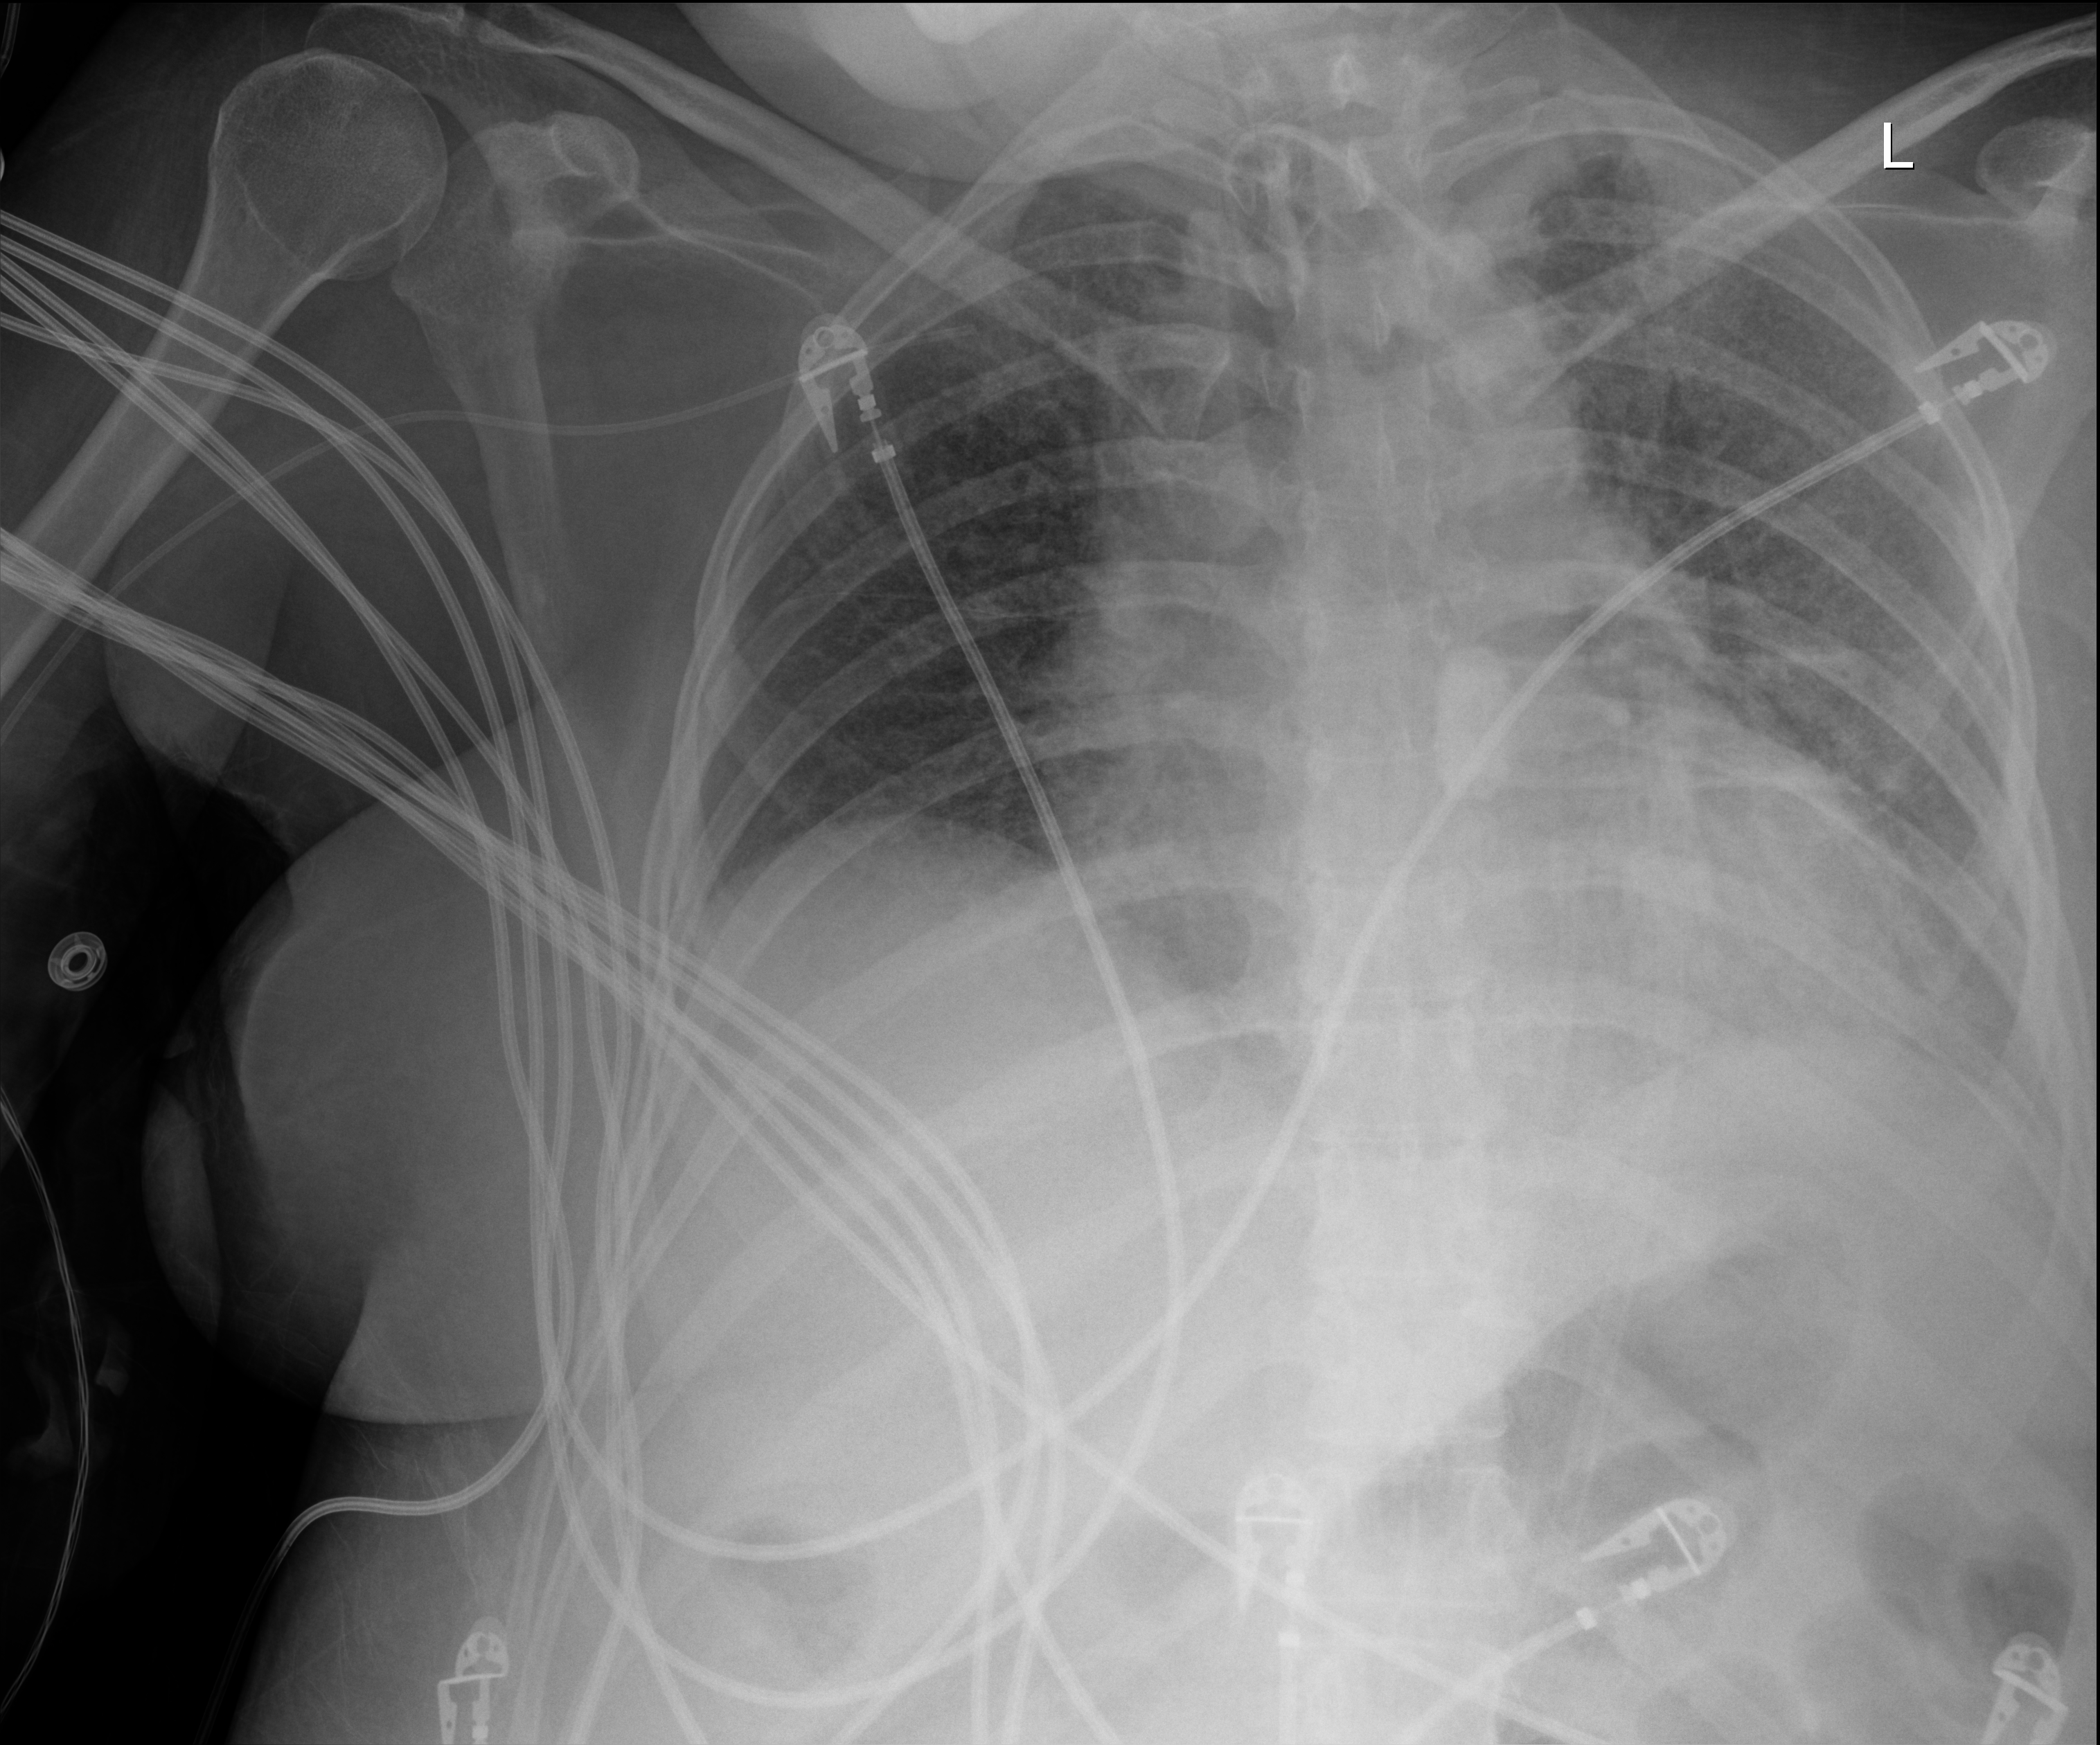
Chest X-ray (portable); anteroposterior (AP) projection. Patient hospitalised with COVID-19; female, aged 18–59 years.
Hospital-stay facts (about this admission, not read from this image; timing relative to this image not recorded):
- mechanically ventilated during this hospital stay: yes